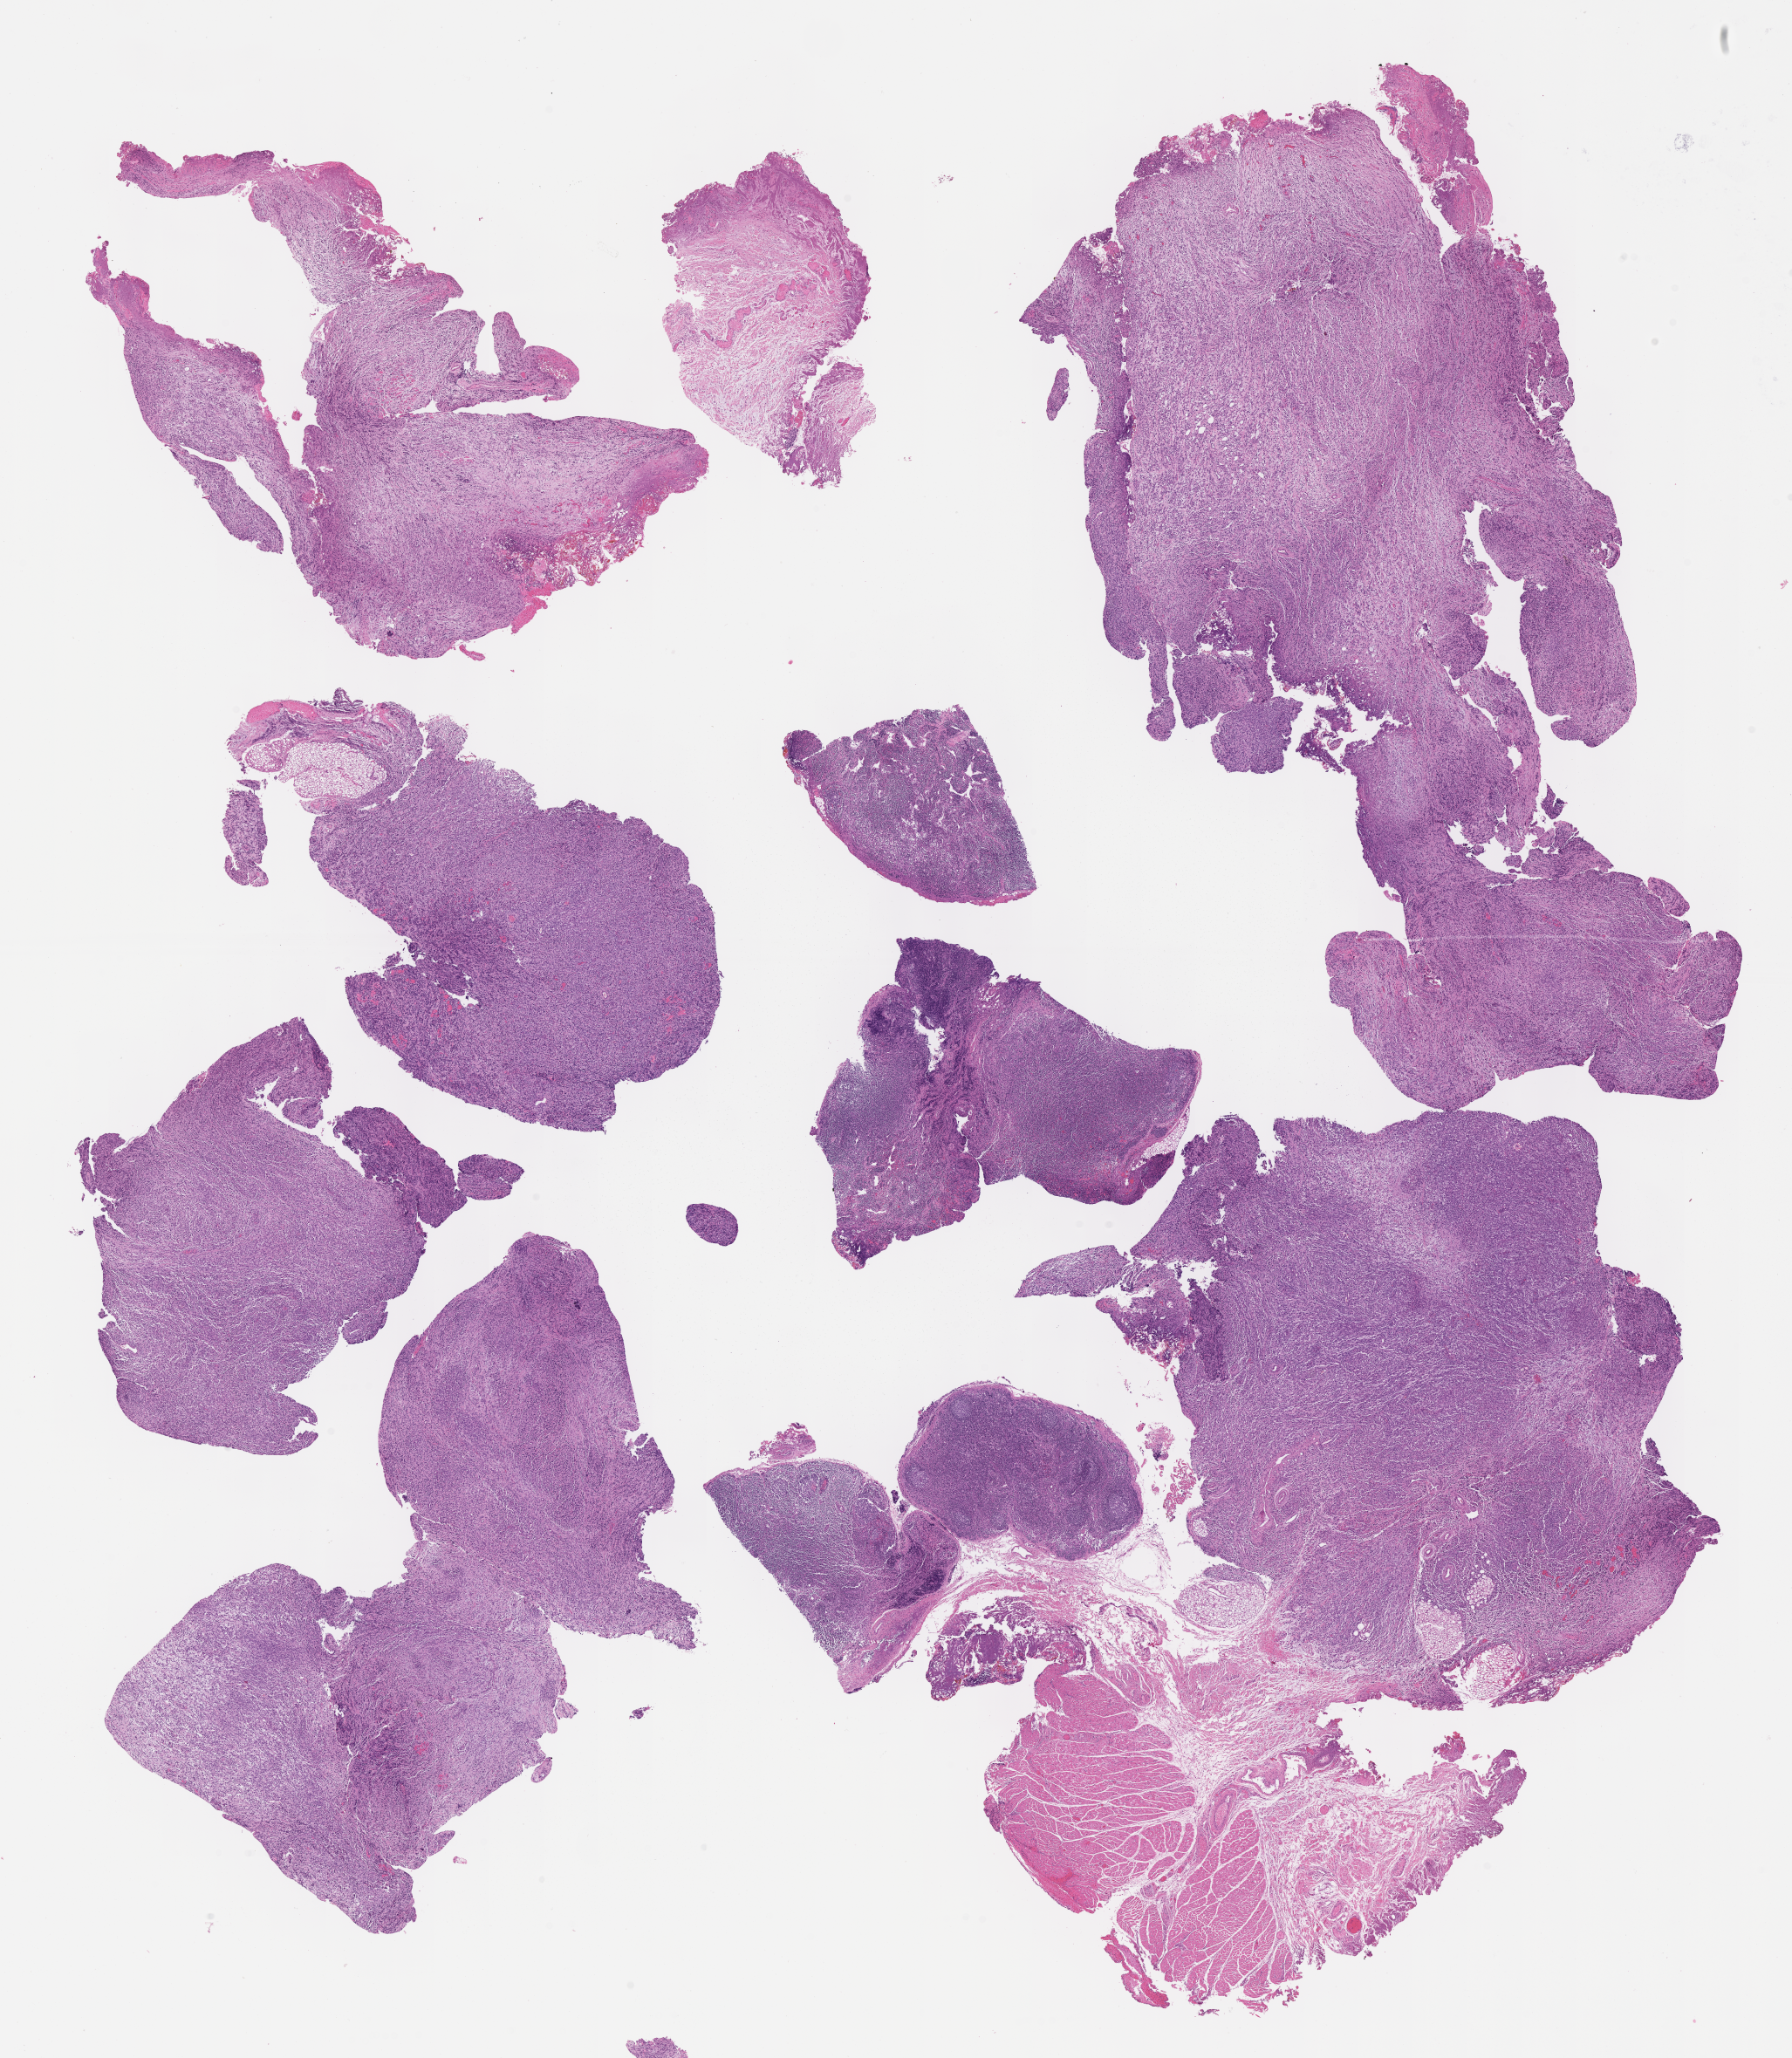
Whole-slide image, hematoxylin and eosin (H&E) stain of tumor tissue — shown as a low-resolution overview of the whole scanned area (about 16.6 x 19.1 mm), formalin-fixed, paraffin-embedded (FFPE) tissue, site: parapharyngeal. Male patient, age at diagnosis 0.1 years.
Stage (as recorded): 4. Metastatic status at presentation (as recorded): metastatic (confirmed). Diagnosis: rhabdomyosarcoma; histological classification: spindle cell rhabdomyosarcoma.